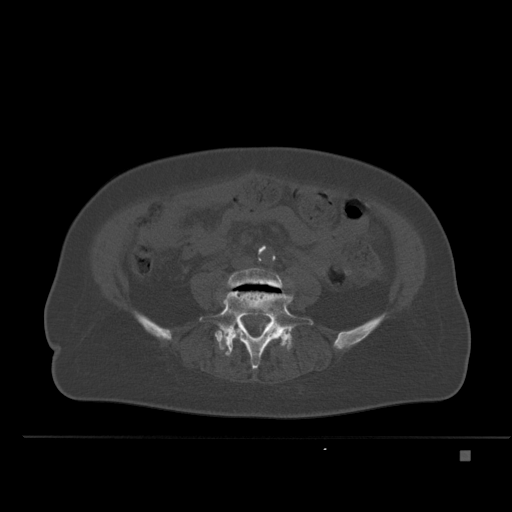
CT including the spine, one axial slice. Position 166 of 477 along the scan axis. Bone window (W 1800 / L 400 HU). 1.5 mm slice thickness. 512 × 512 image matrix, field of view 422 × 422 mm. Patient: female, 74 years. From the clinical record (not read from this slice): primary cancer: colon.
Structures marked on this image (semi-automatically segmented with operator editing):
- L4 vertebra: bounding box <224,268,284,338> (left, top, right, bottom; pixels)
- L5 vertebra: <200,292,313,370>